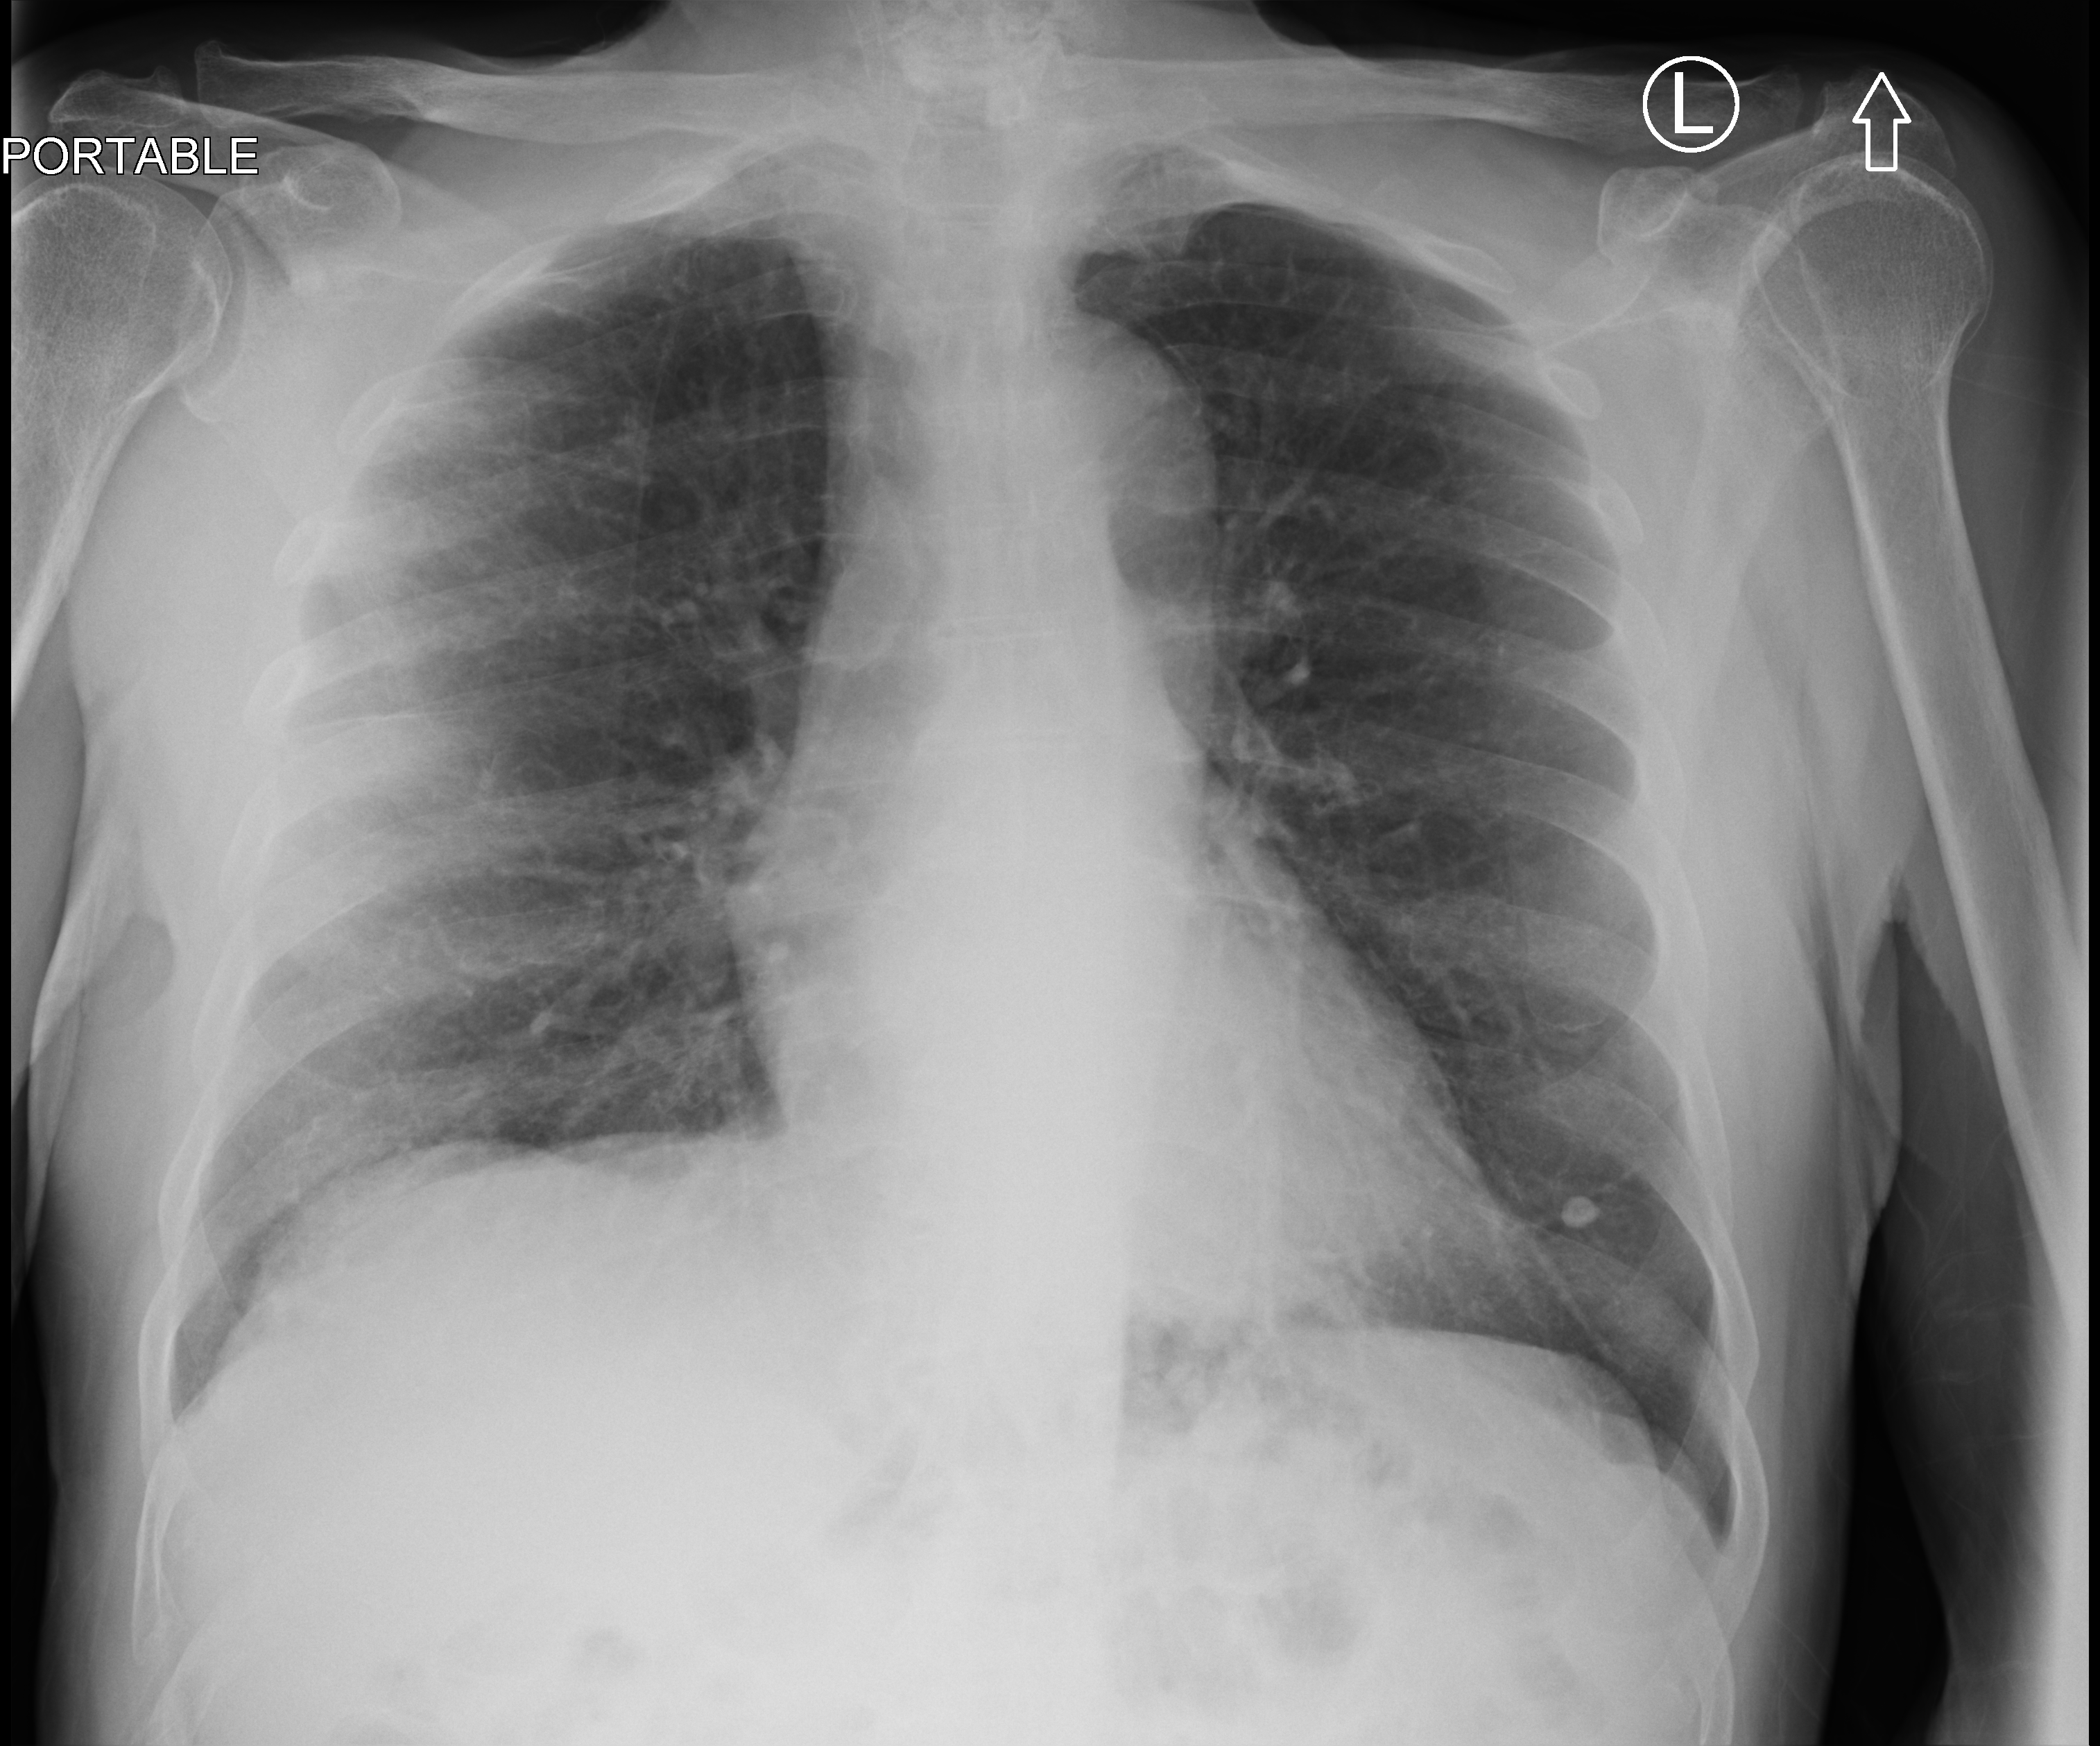
Chest X-ray (portable), anteroposterior (AP) projection. Male patient hospitalised with COVID-19, age 75–90 years.
Admission-level facts for this patient (not findings on this image; timing relative to this image not recorded): admitted to intensive care during this hospital stay: no; mechanically ventilated during this hospital stay: no.